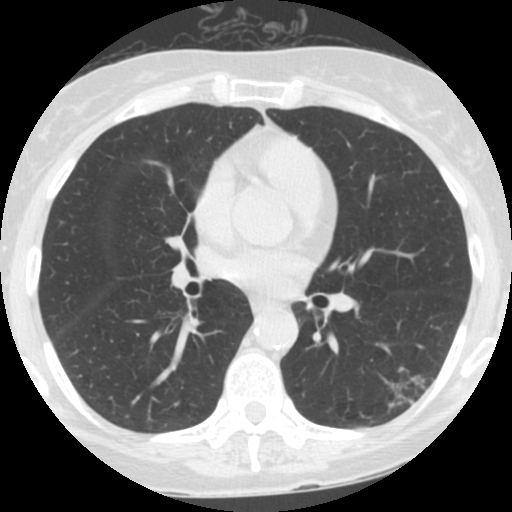
Low-dose screening chest CT, one axial slice. Slice 71 of 152 in the series (ordered by position). 120 kVp. Lung window (W 1500 / L -600 HU). 2.5 mm slice thickness. 512 × 512 image matrix, field of view 280 × 280 mm.
Annotated regions visible in this slice (outlined manually by an expert reader):
- lesion 1 (tumor, lower lobe of left lung): bounding box (x1, y1, x2, y2) in pixels: (391, 372, 427, 410)